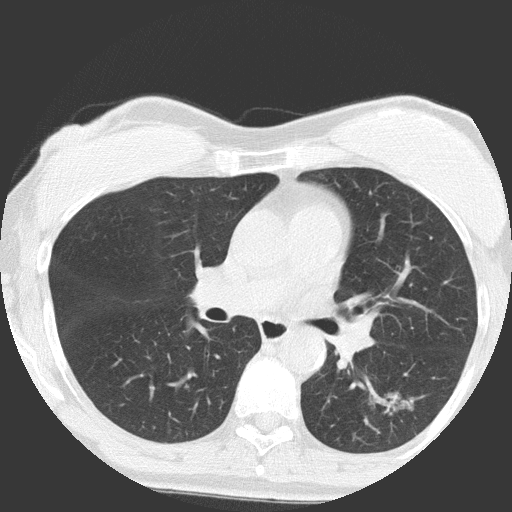
Low-dose screening chest CT, axial slice; baseline annual screen; lung window (W 1500 / L -600 HU); lung (sharp) reconstruction kernel (FC51); 512 × 512 image matrix, field of view 300 × 300 mm. Female participant, aged 64 years at enrolment. Former smoker at enrolment.
Expert reader's lesion annotation, bounding box (x1, y1, x2, y2) in pixels: (354, 376, 438, 451). Screening reader's record for this exam (one nodule recorded; not confirmed to be the boxed lesion): non-calcified nodule or mass ≥4 mm, right upper lobe, 4 × 4 mm, poorly defined margins, ground glass attenuation. Note: the box lies in the patient's left hemithorax on this image, whereas the reader's record names the right lung; they may be different findings. Lung cancer was diagnosed 932 days after this screen: adenocarcinoma, NOS, left lower lobe, moderately differentiated (G2), stage IA (AJCC 6th edition), 17 mm at pathology.